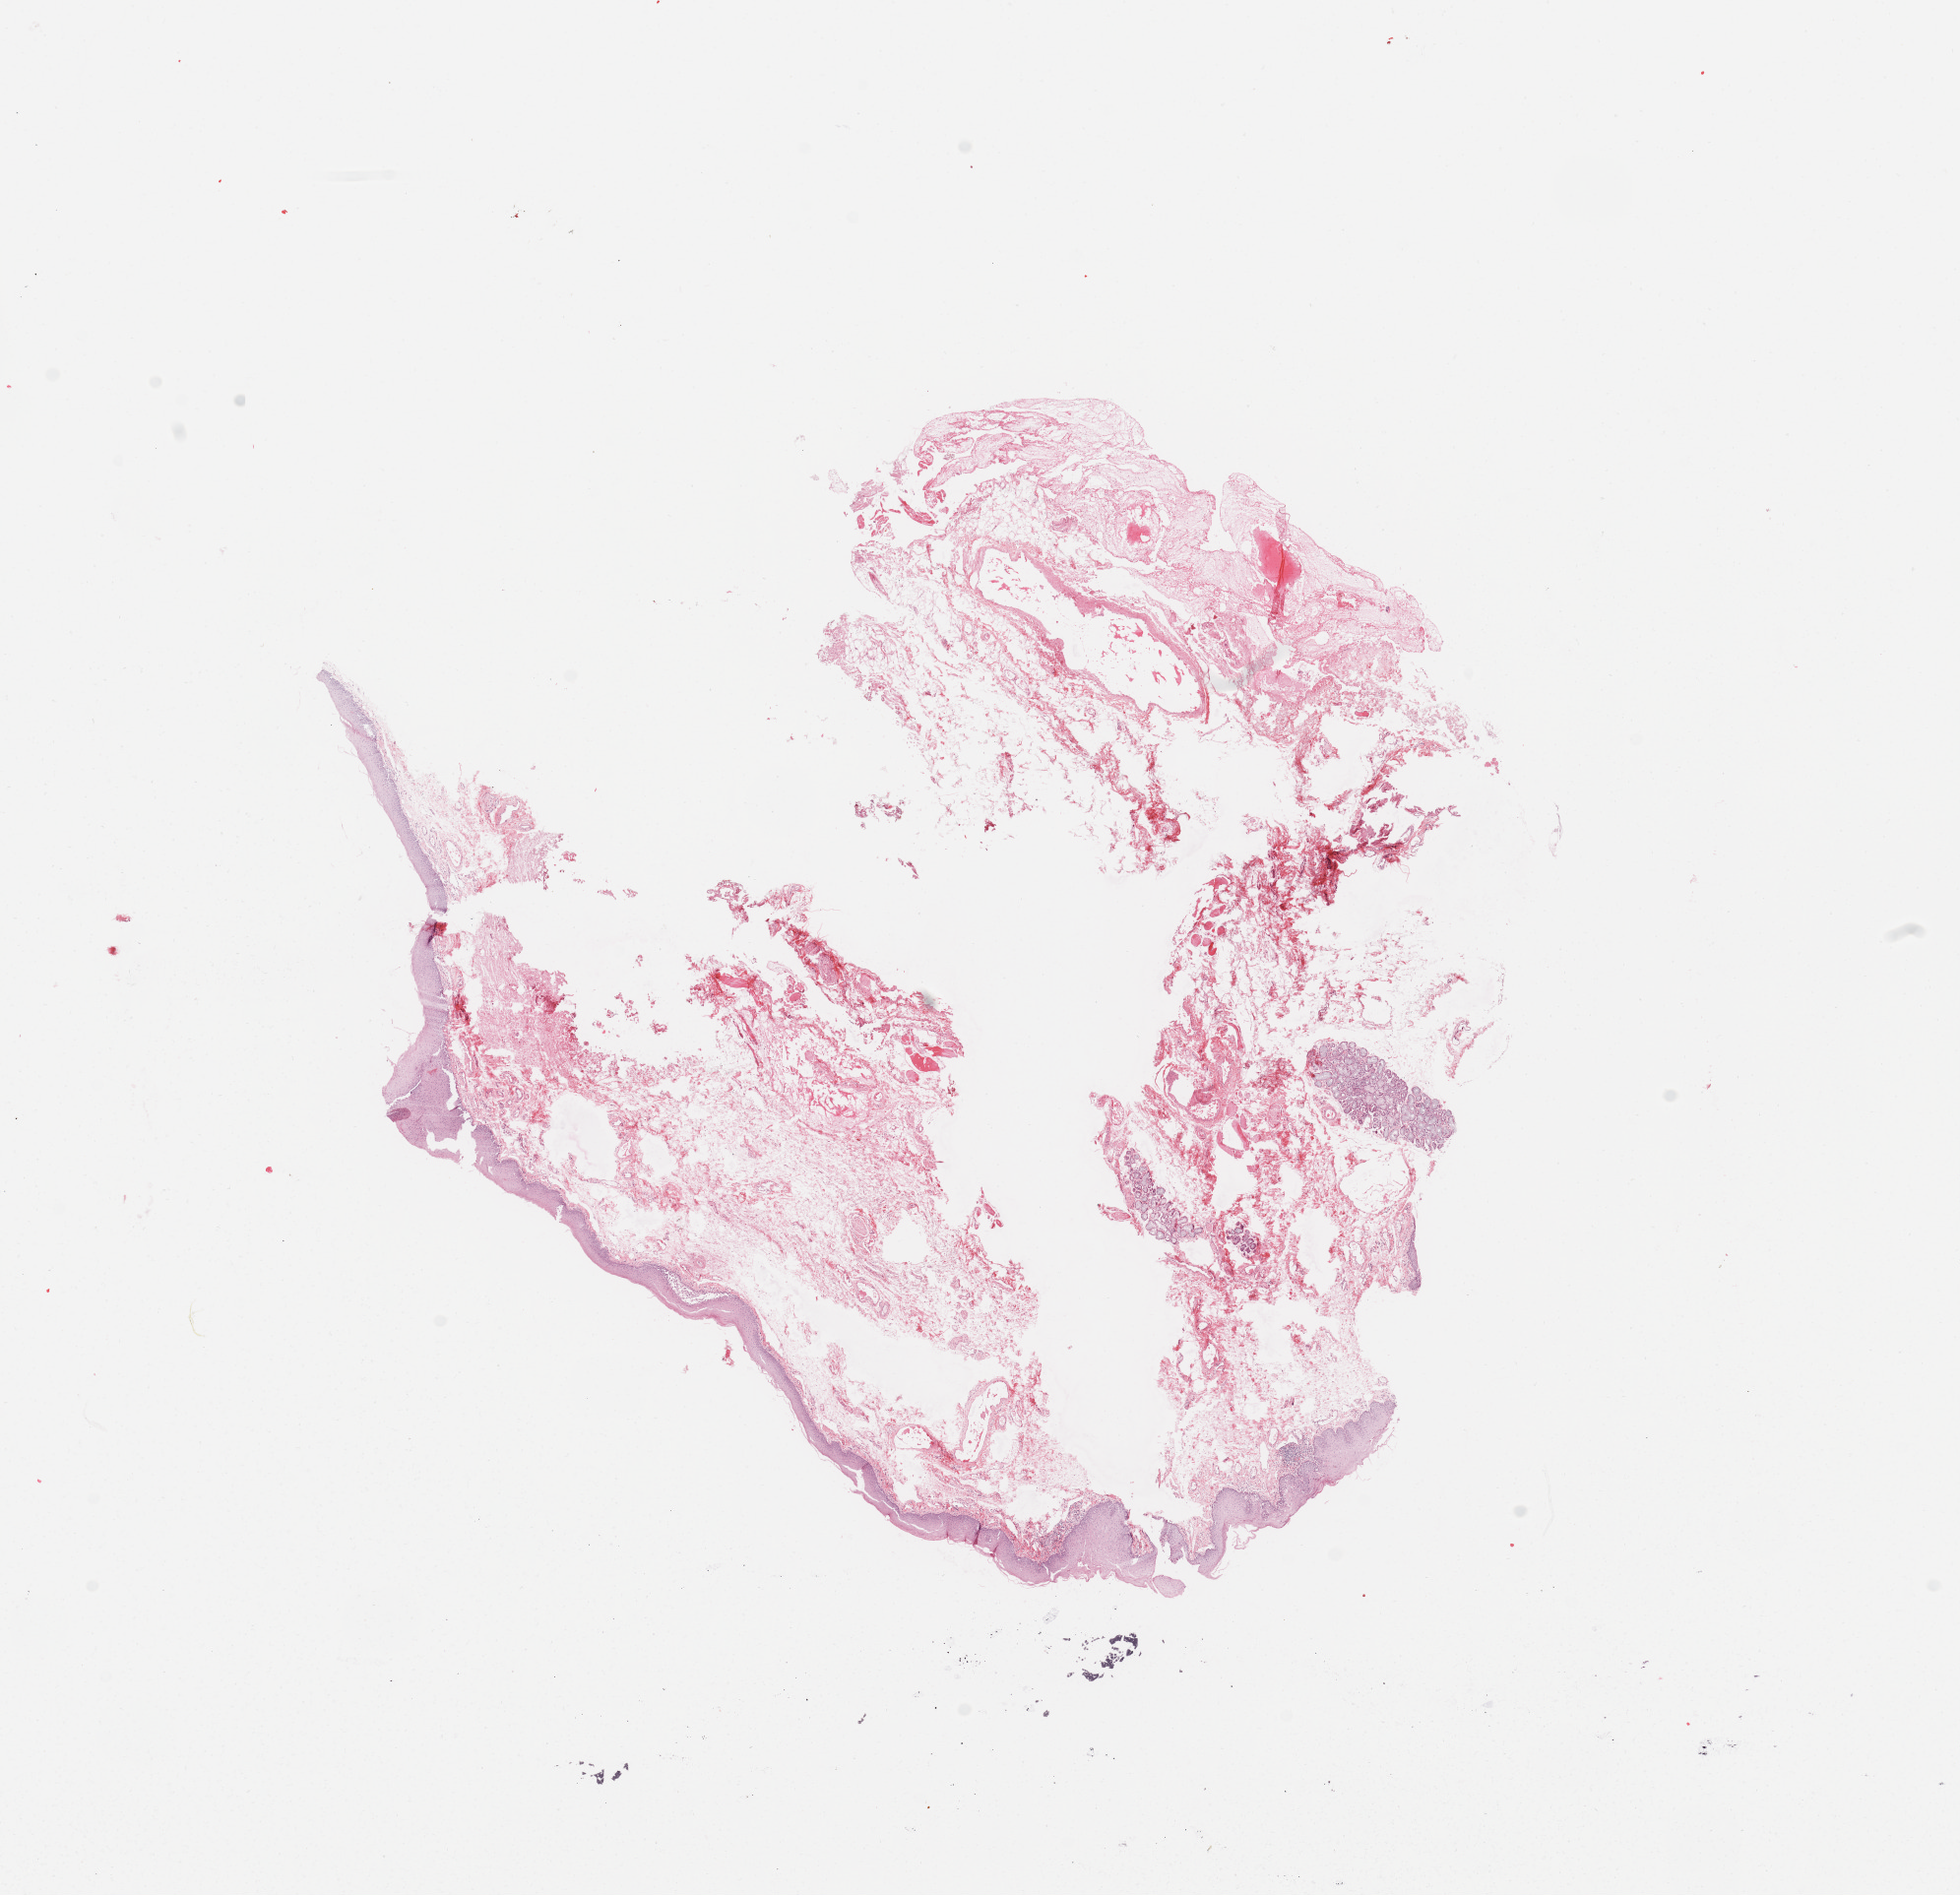
Whole-slide histology image, Hematoxylin and eosin (H&E) stained, whole scanned area (about 15.8 x 15.2 mm) shown as a low-resolution overview, normal (non-tumour) tissue sample, sampled site: supraglottis. 59-year-old male patient.
• this section: normal (non-tumour) tissue from the same patient
• patient diagnosis: Squamous cell carcinoma, NOS (head, face or neck, NOS)